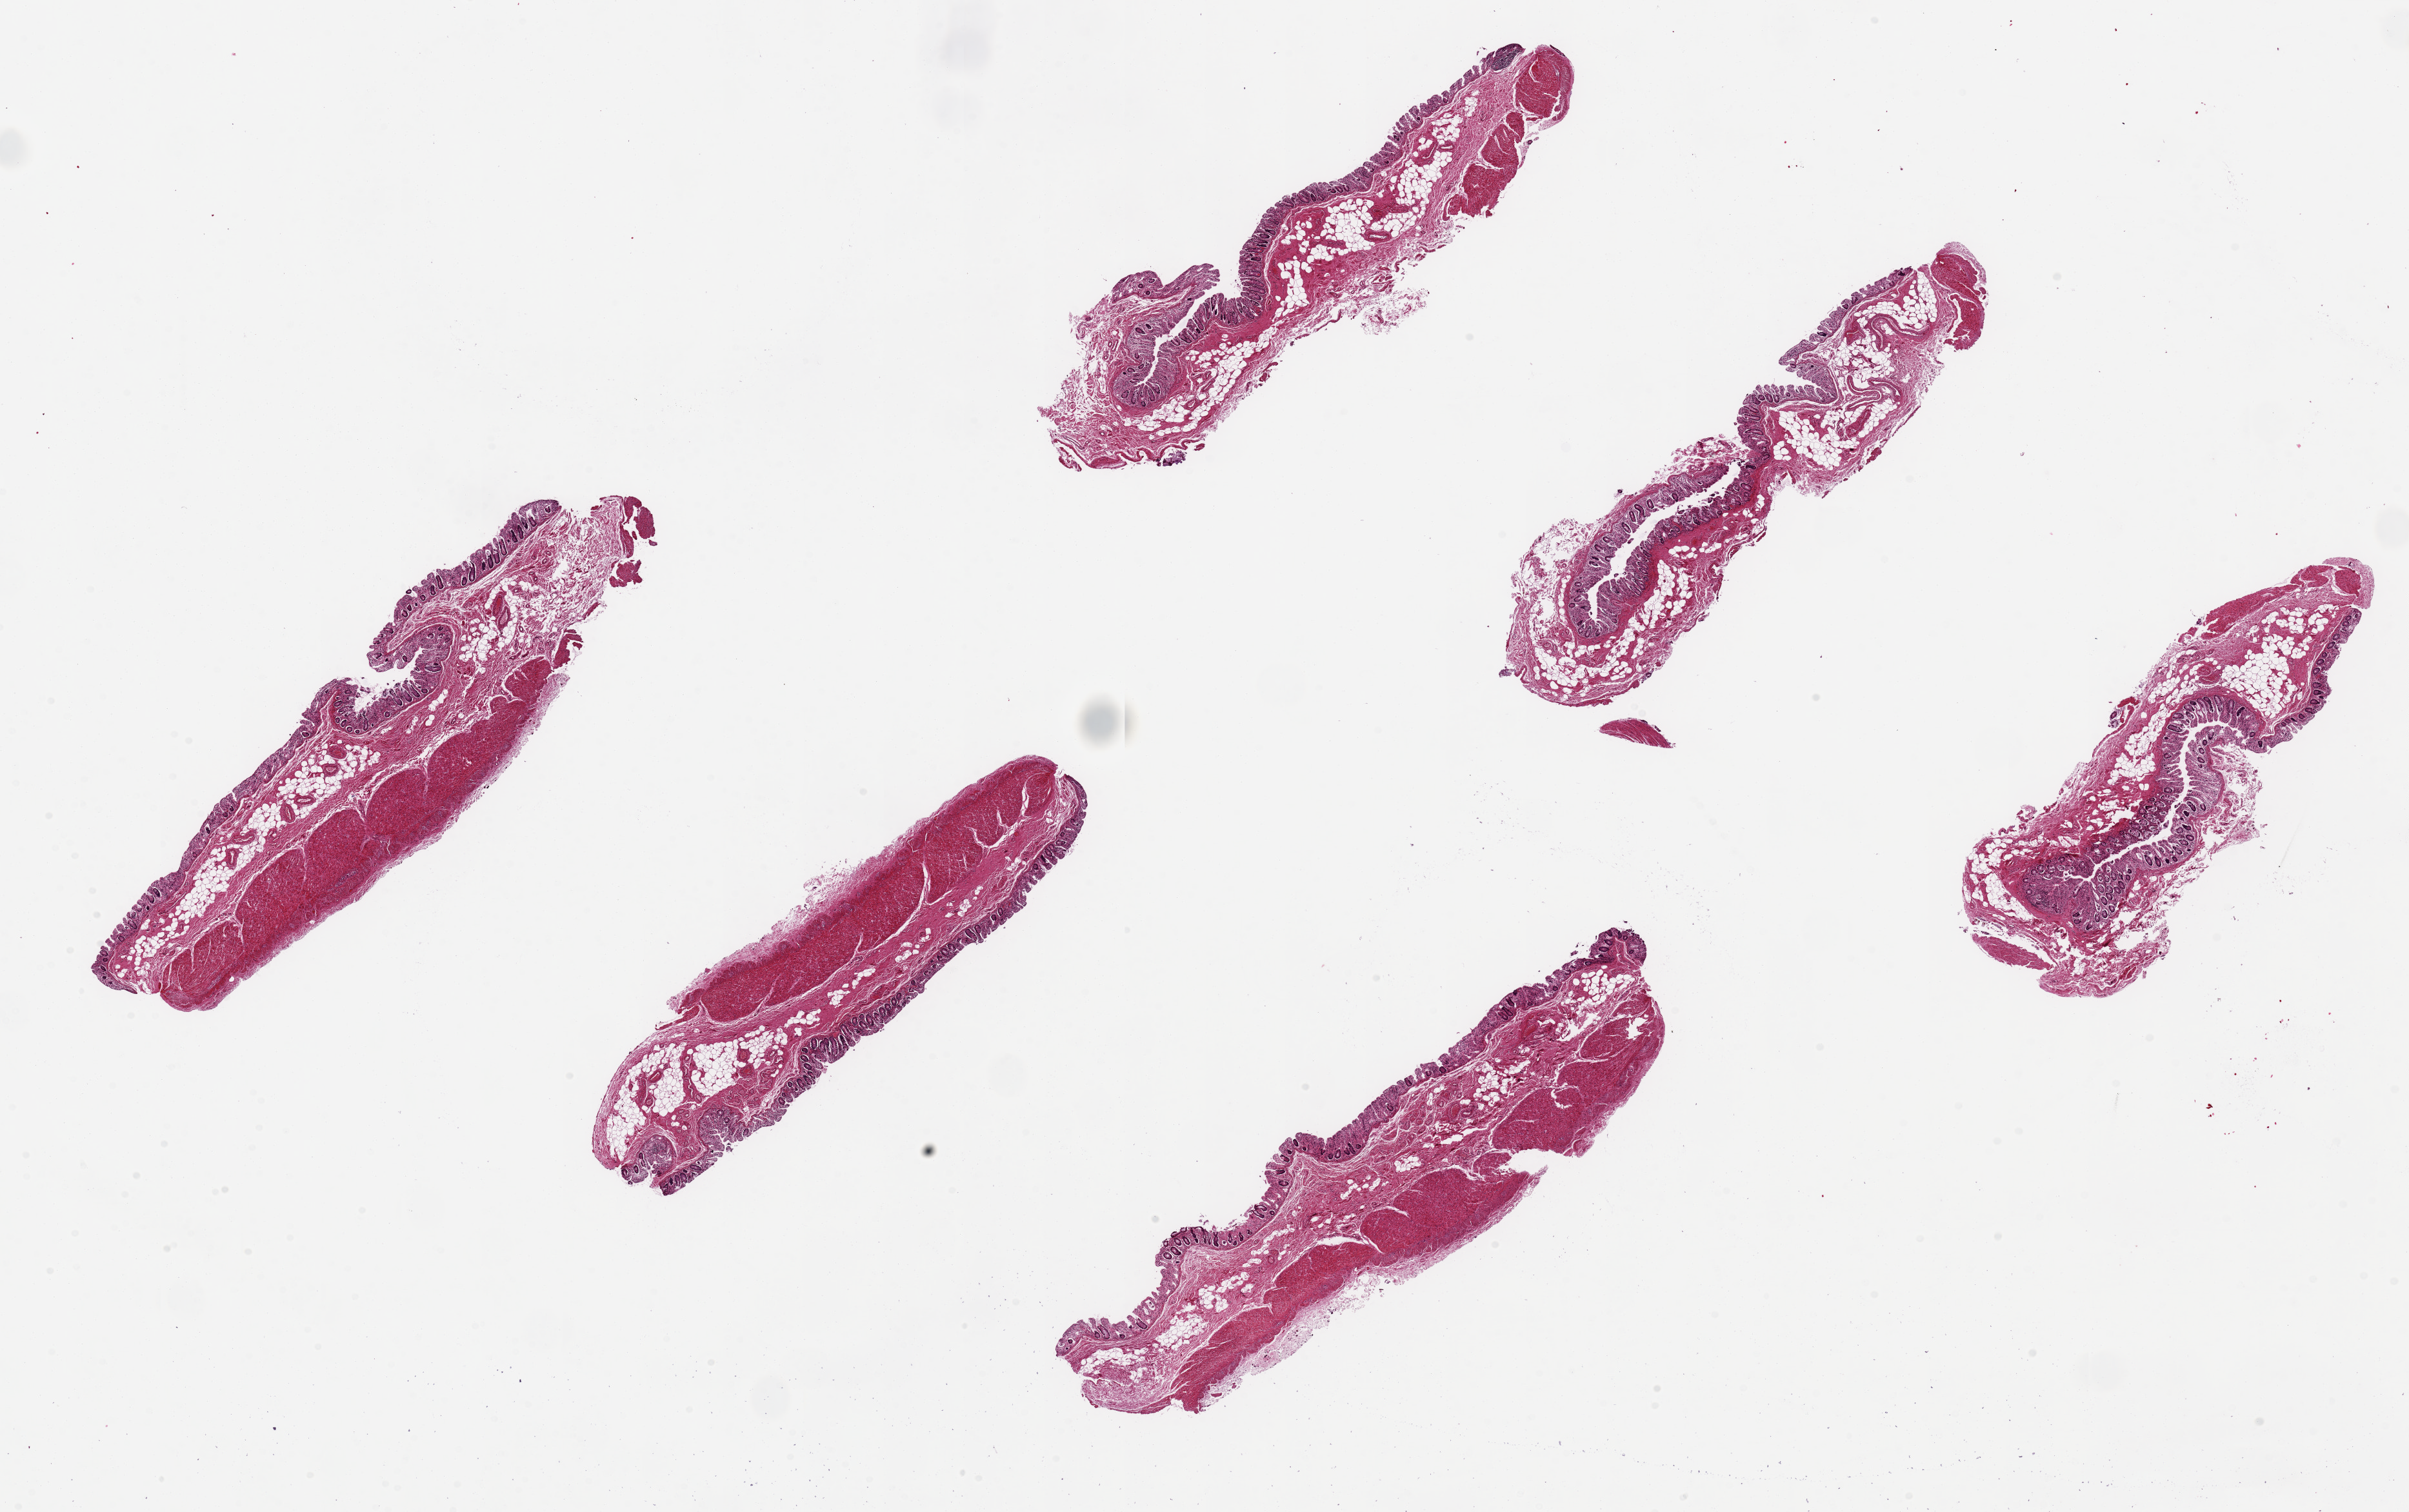
Digitized haematoxylin and eosin-stained section, brightfield, a low-resolution overview of the entire scanned area, about 29.5 x 18.5 mm (acquisition: 20x scan), PAXgene-fixed paraffin-embedded (PFPE) section, sampled site (target tissue): transverse colon, donor tissue sample. Male donor.
Pathologist's review note for this sample: 6 pieces up to 9x2 mm; mucosa on all (but autolyzed); muscularis varies in extent; submucosa heavily adiposed.